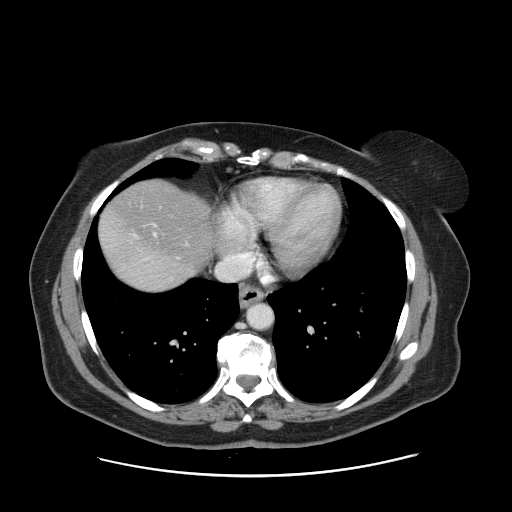
Contrast-enhanced abdominal CT, one axial slice. Slice 143 of 161 in the series (ordered by position). 120 kVp. Intravenous contrast given. Soft-tissue window (W 400 / L 40 HU). 2.5 mm slice thickness. 512 × 512 image matrix, field of view 398 × 398 mm. Female patient, age 62 years. Case-level facts recorded for this patient, not image findings: diagnosis: colorectal cancer liver metastases, imaged before liver resection; multiple liver metastases: no.
Structures marked on this image (manually delineated by an expert):
- hepatic veins: bounding box [x1, y1, x2, y2] px = [133, 233, 157, 259]
- liver: [99, 181, 211, 291]
- planned liver remnant (the part of the liver to remain after resection): [100, 181, 213, 272]